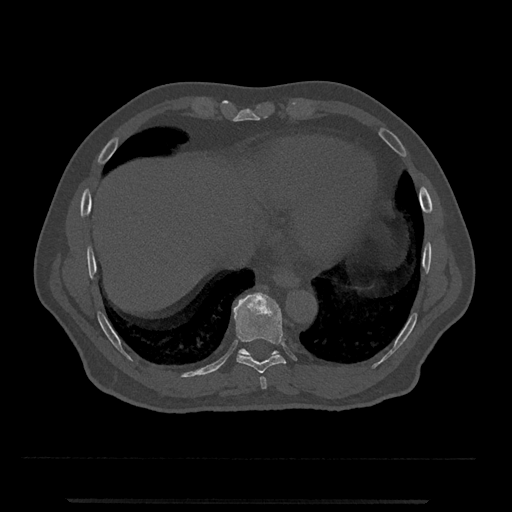
CT including the spine, one axial slice. Position 562 of 797 along the scan axis. 120 kVp. Bone window (W 1800 / L 400 HU). 0.5 mm slice thickness. 512 × 512 image matrix, field of view 419 × 419 mm. Male patient, age 63 years. Case-level facts recorded for this patient, not image findings: primary cancer: prostate.
Structures marked on this image (semi-automatically segmented with operator editing):
- T10 vertebra: bounding box <239,348,279,358> (left, top, right, bottom; pixels)
- T8 vertebra: <260,376,267,389>
- T9 vertebra: <233,293,286,374>